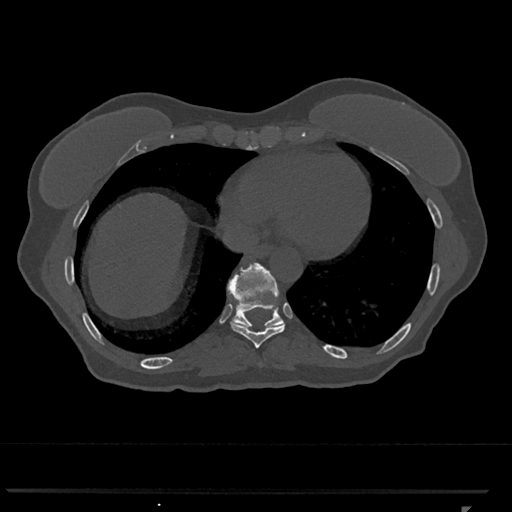
CT including the spine, one axial slice. Position 602 of 793 along the scan axis. 120 kVp. Bone window (W 1800 / L 400 HU). 512 × 512 image matrix, field of view 380 × 380 mm. Patient: female, 62 years. From the clinical record (not read from this slice): primary cancer: renal.
Outlined on this slice (semi-automatic segmentation, software-assisted and operator-edited):
- T10 vertebra: bounding box <227,263,284,327> (left, top, right, bottom; pixels)
- T9 vertebra: <230,306,286,349>